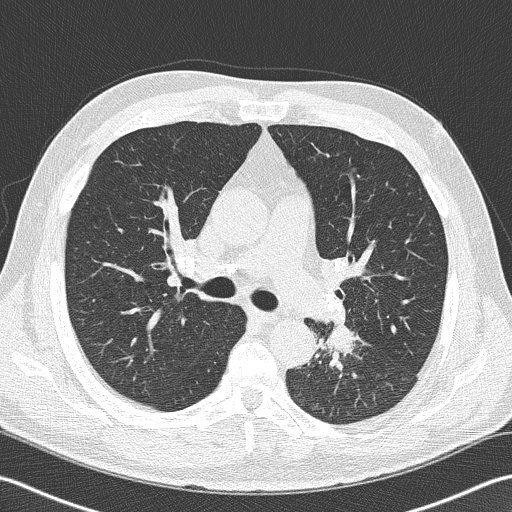
Low-dose screening chest CT, axial slice. Second annual screen. Lung window (W 1500 / L -600 HU). Slice 62 of 170 in the series. 512 × 512 image matrix. Male, age 57 years at enrolment.
Expert-annotated lung lesion, bounding box [x1, y1, x2, y2] px = [294, 312, 374, 386]. Screening reader's record for this exam (one nodule recorded; not confirmed to be the boxed lesion): non-calcified nodule or mass ≥4 mm, left lower lobe, 40 × 30 mm, spiculated (stellate) margins, soft tissue attenuation, pre-existing on the prior screen: no. Official screen result: positive, other. Later outcome: lung cancer diagnosed 9 days after this screen — squamous cell carcinoma, NOS, left lower lobe, moderately differentiated (G2), stage IIIB (AJCC 6th edition), 38 mm at pathology.